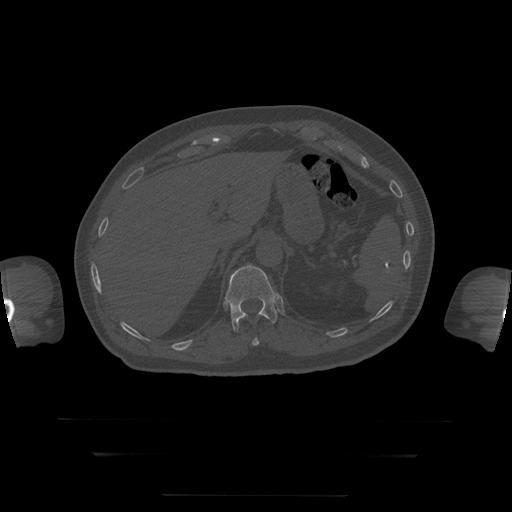
CT including the spine, one axial slice. Slice 82 of 397 in the series (ordered by position). Reconstruction kernel STANDARD. Bone window (W 1800 / L 400 HU). 1.25 mm slice thickness. 512 × 512 image matrix. Patient age 73 years. From the clinical record (not read from this slice): primary cancer: prostate.
Structures marked on this image (semi-automatically segmented with operator editing):
- T11 vertebra: bounding box [x1, y1, x2, y2] px = [243, 315, 260, 346]
- T12 vertebra: [226, 265, 280, 332]